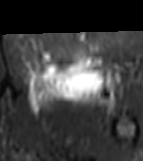
MRI of an extremity soft-tissue mass, one axial slice; position 41 of 81 along the scan axis; STIR; MR volume resampled by the dataset authors to the PET/CT grid (not the native acquisition matrix); 3.27 mm slice thickness; 143 × 161 image matrix, field of view 140 × 157 mm. Female patient. Case-level facts recorded for this patient, not image findings: histological type: myxofibrosarcoma; grade: intermediate; site of the primary tumour: left thigh.
Annotated regions visible in this slice (expert contour drawn on MRI and transferred to this co-registered scan by the dataset authors):
- gross tumour volume including surrounding oedema: box from (x=24, y=56) to (x=118, y=111) px
- gross tumour volume (mass): (x=37, y=56)–(x=100, y=98)